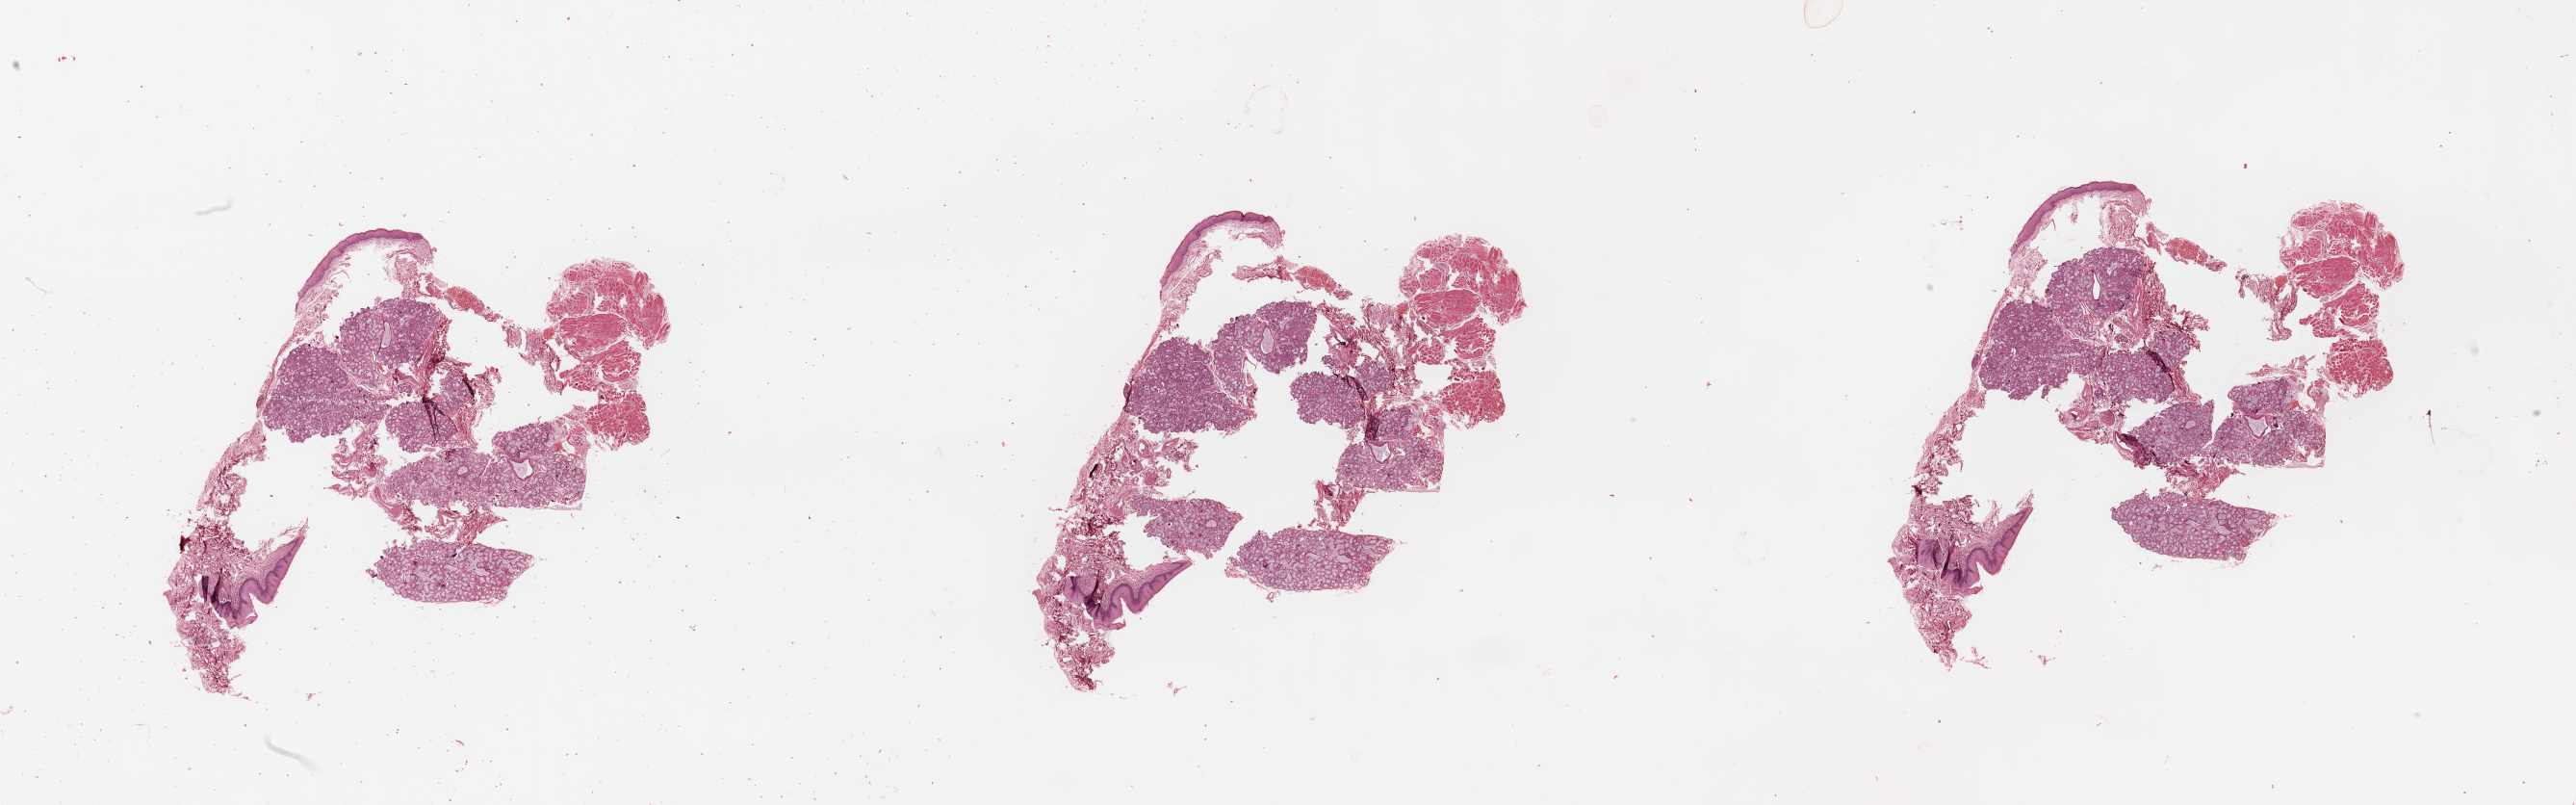
Hematoxylin and eosin (H&E) stained whole-slide image — whole scanned area (about 42.3 x 13.2 mm) shown as a low-resolution overview; normal (non-tumour) tissue sample, head and neck. Male, 64 y/o.
This section: normal (non-tumour) tissue from the same patient. Patient diagnosis: Squamous cell carcinoma, NOS (larynx, NOS).